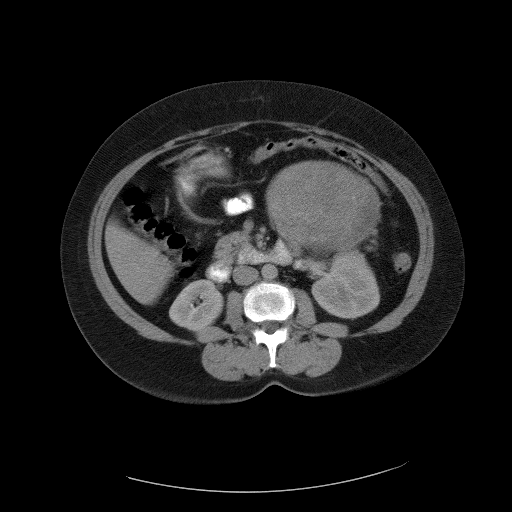
Contrast-enhanced abdominal CT, one axial slice; position 55 of 90 along the scan axis; reconstruction kernel FC01; intravenous contrast given; soft-tissue window (W 400 / L 40 HU); 512 × 512 image matrix. Patient: female, 55 years. From the clinical record (not read from this slice): diagnosis: adrenocortical carcinoma; tumour side: left adrenal; tumour size at pathology: 22 cm; Ki-67 index: 10 %; stage (as recorded): 3.
Outlined on this slice (semi-automatically segmented with operator editing):
- mass: bounding box [x1, y1, x2, y2] px = [267, 162, 378, 254]